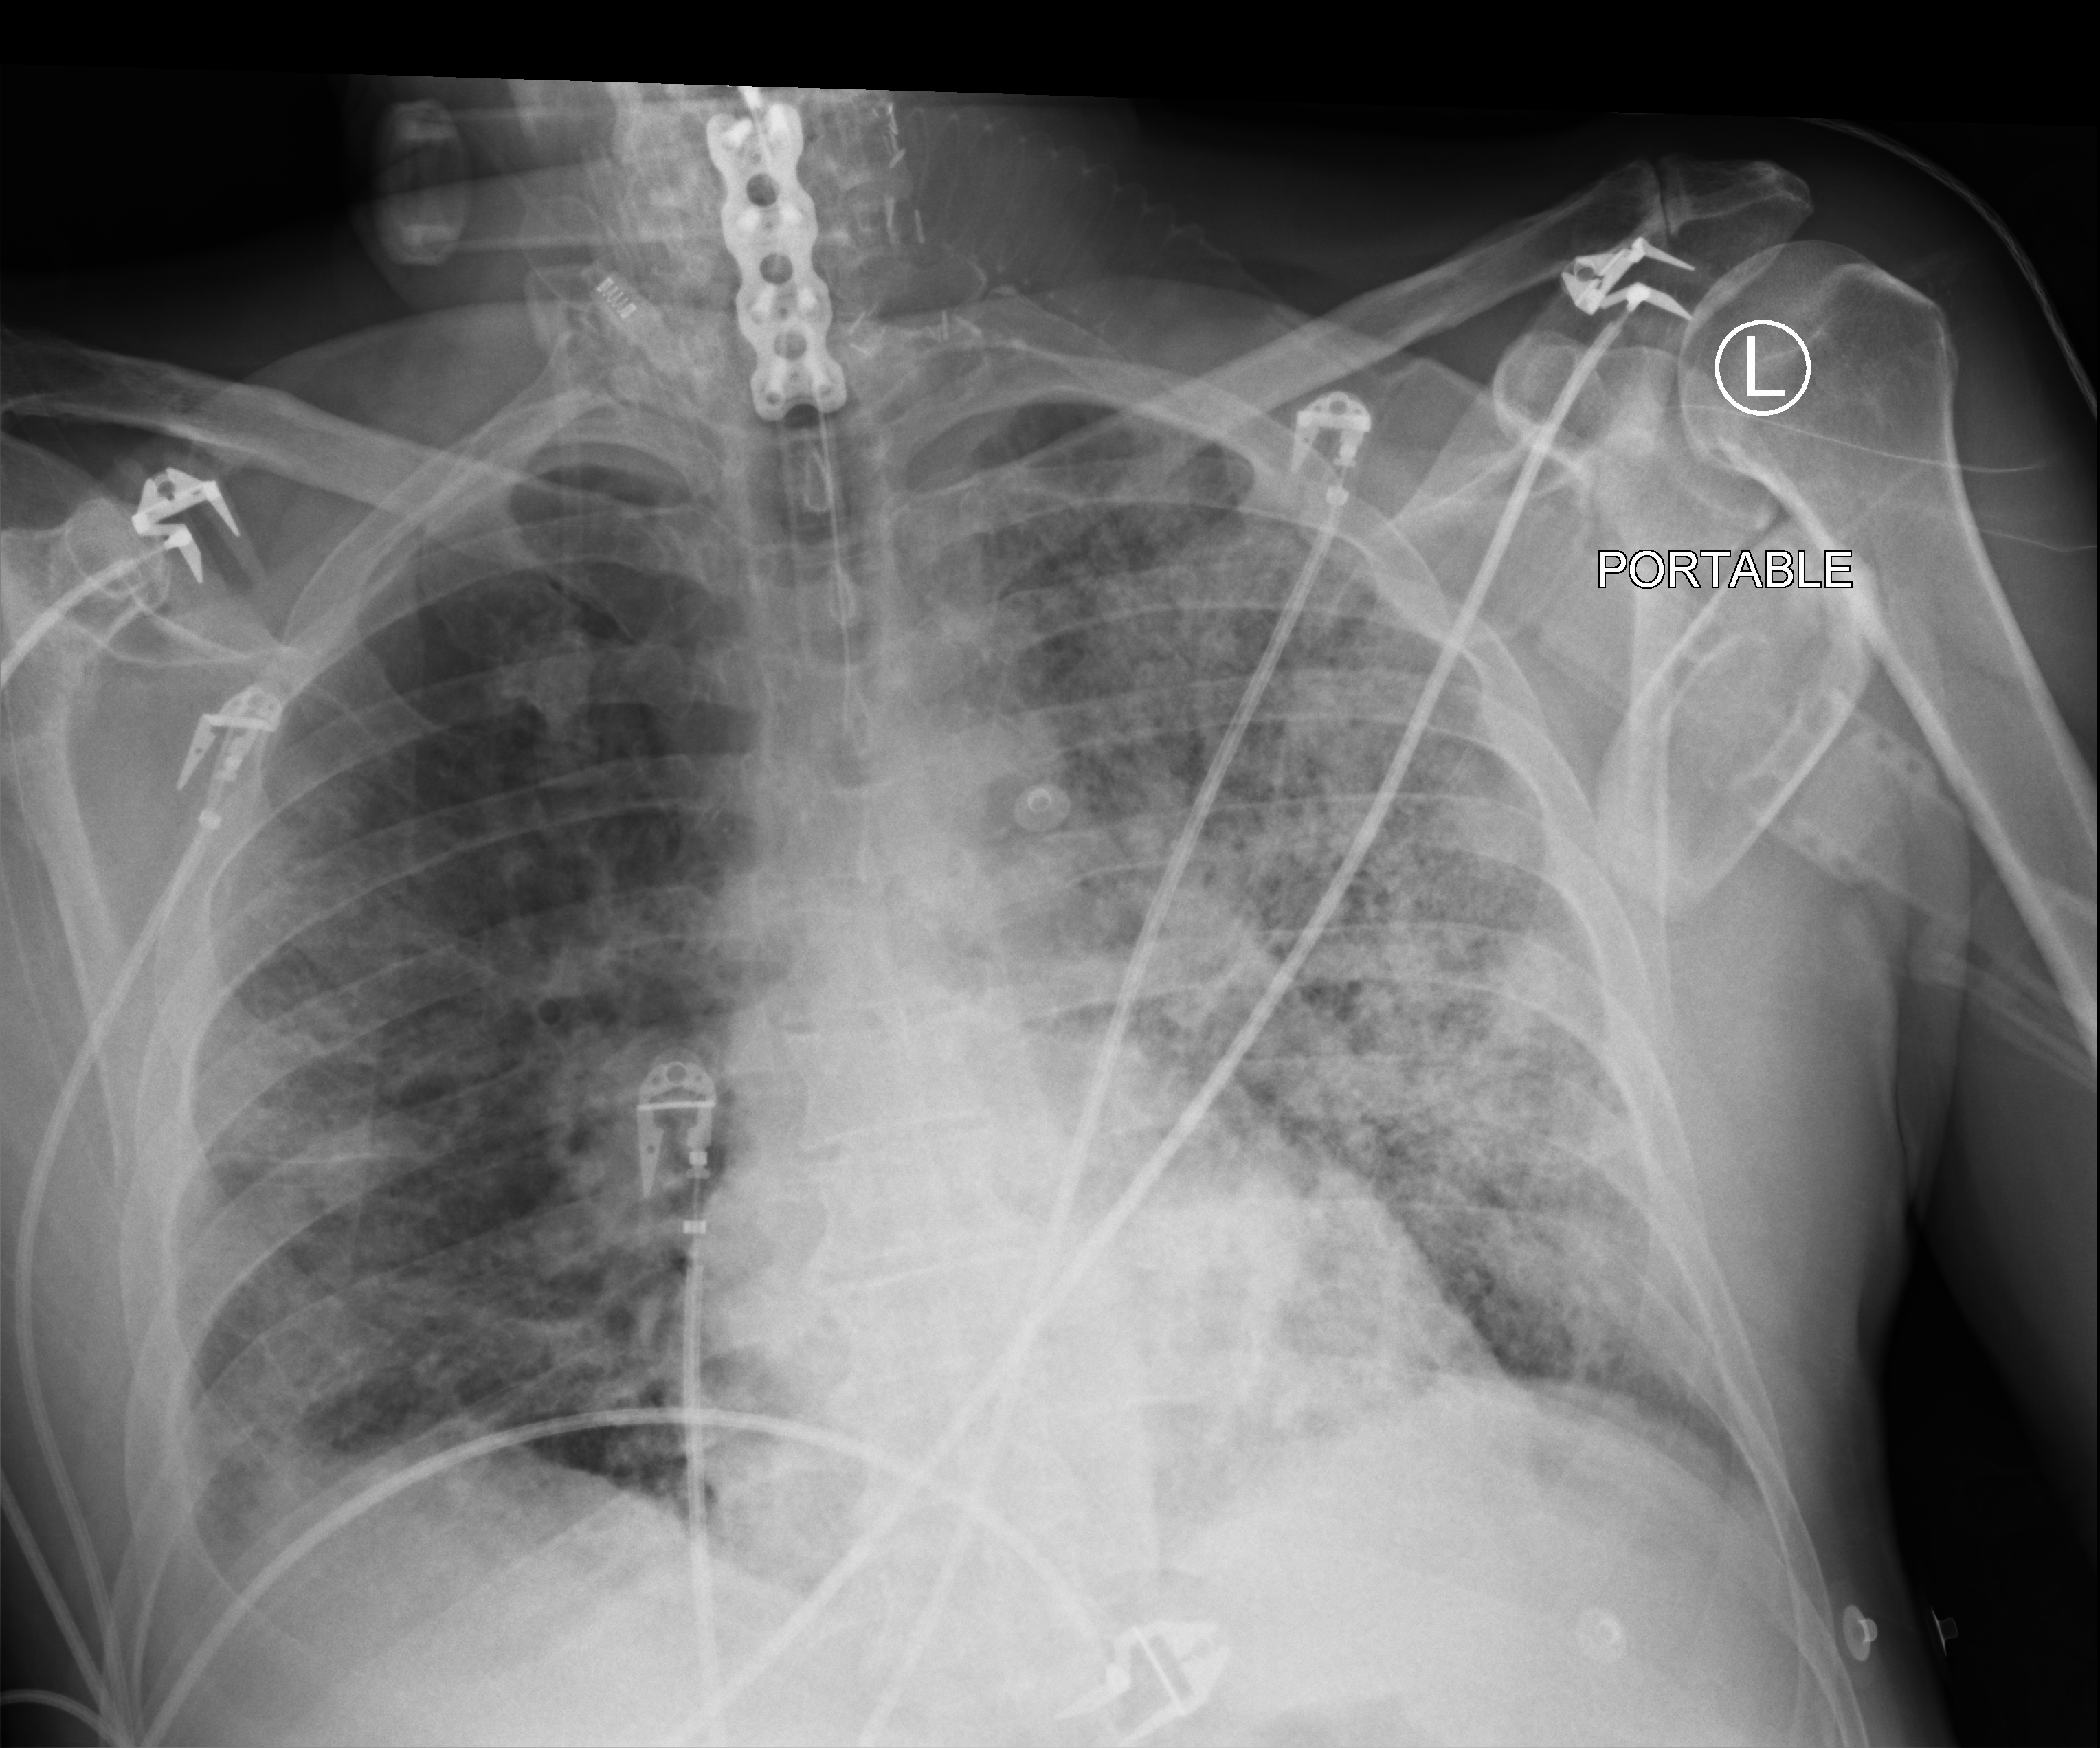
Bedside chest radiograph (computed radiography). Patient hospitalised with COVID-19; male, aged 60–74 years.
Admission-level facts for this patient (not findings on this image; timing relative to this image not recorded):
- mechanically ventilated during this hospital stay: yes